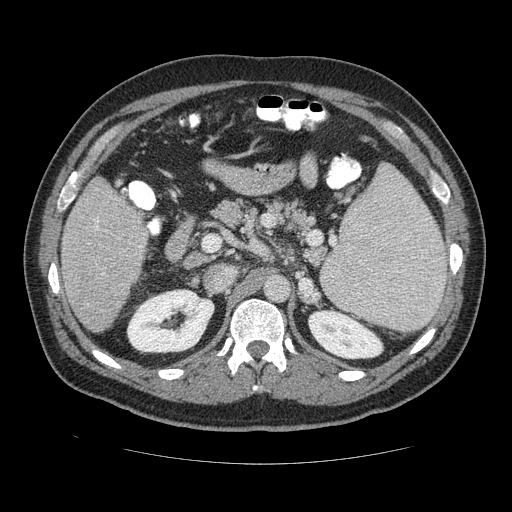
Contrast-enhanced abdominal CT (liver protocol), one axial slice. Position 67 of 113 along the scan axis. Reconstruction kernel STANDARD. 120 kVp. Soft-tissue window (W 400 / L 40 HU). 2.5 mm slice thickness. 512 × 512 image matrix, field of view 400 × 400 mm. From the clinical record (not read from this slice): diagnosis: hepatocellular carcinoma (patient treated with transarterial chemoembolisation; whether this scan precedes or follows treatment is not stated here); TNM stage (as recorded): Stage-II; Child-Pugh class: B; tumour differentiation: moderately differentiated; tumour nodularity: multinodular.
Outlined on this slice (semi-automatic segmentation, software-assisted and operator-edited):
- liver parenchyma outside the tumour (the mass and vessels are separate outlines, so this box may not span the whole liver): bounding box [x1, y1, x2, y2] px = [60, 176, 150, 334]
- liver vessels: [95, 224, 104, 276]